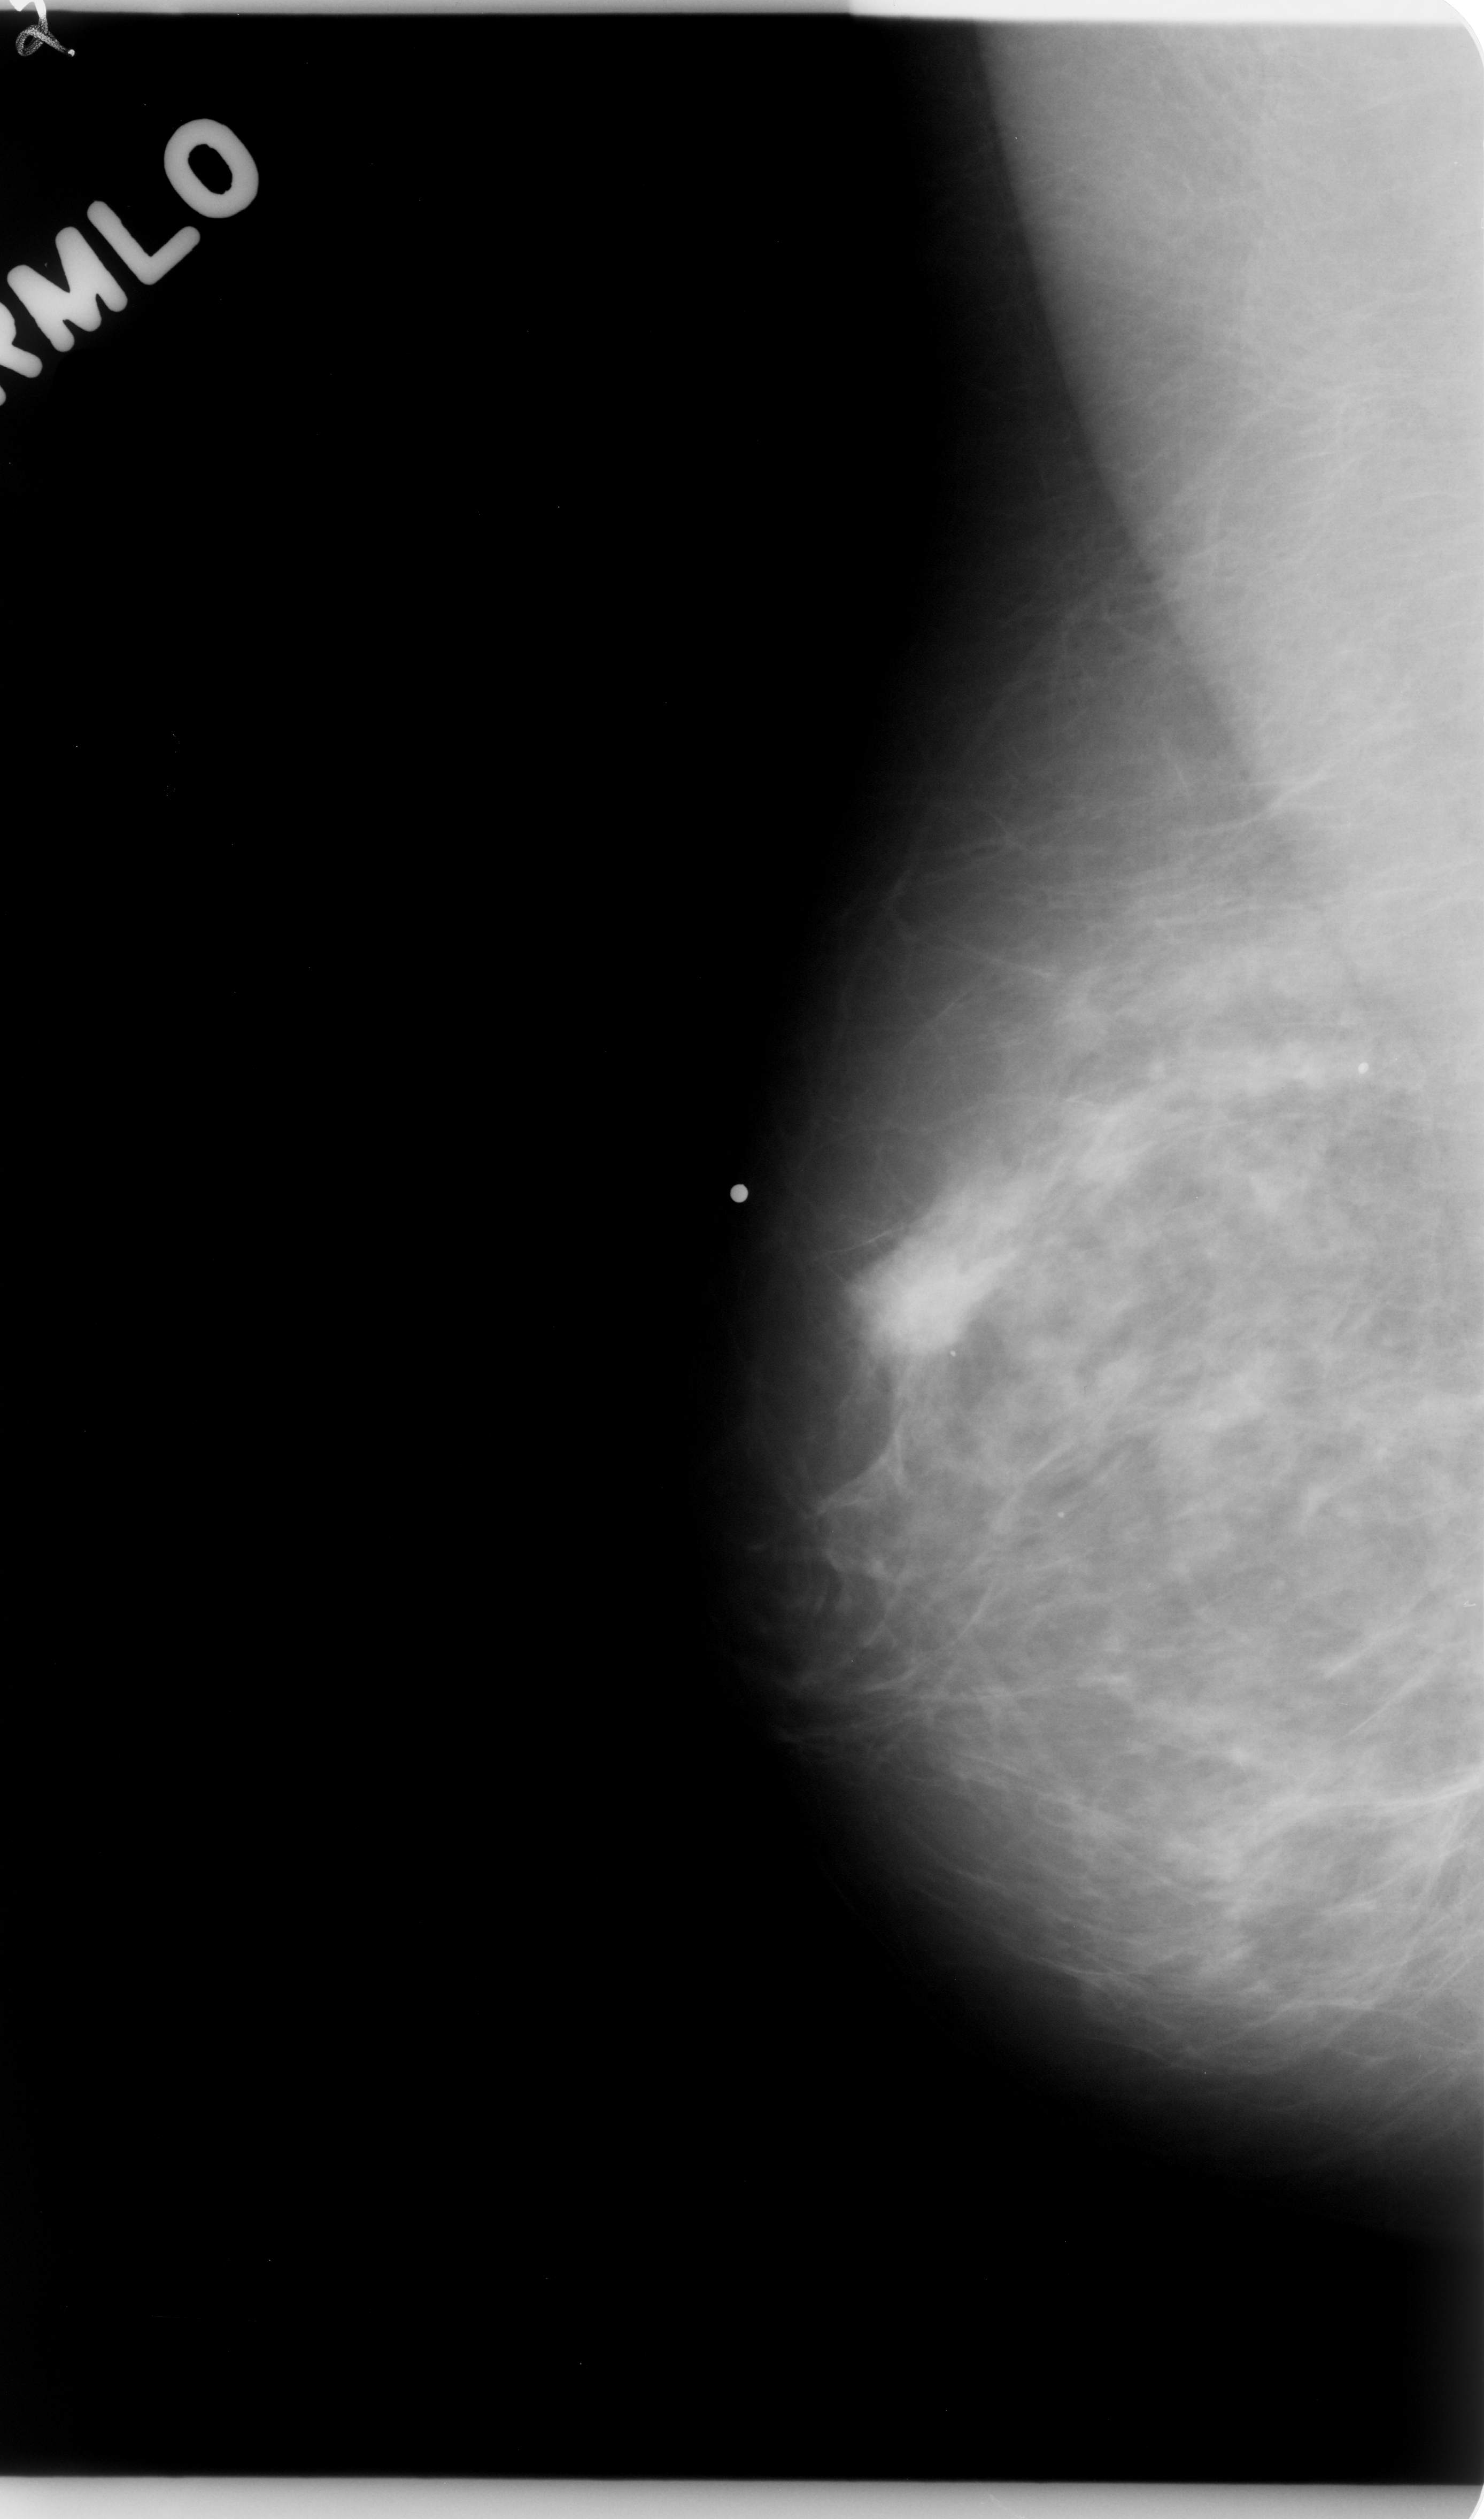
Digitized screen-film mammogram; right breast; mediolateral oblique (MLO) view; BI-RADS breast density category 2 (scale 1–4).
- Finding: mass, shape irregular, margins microlobulated; BI-RADS assessment category 5; subtlety rating 5 on a 1 (subtle) to 5 (obvious) scale; pathology (as recorded): malignant.